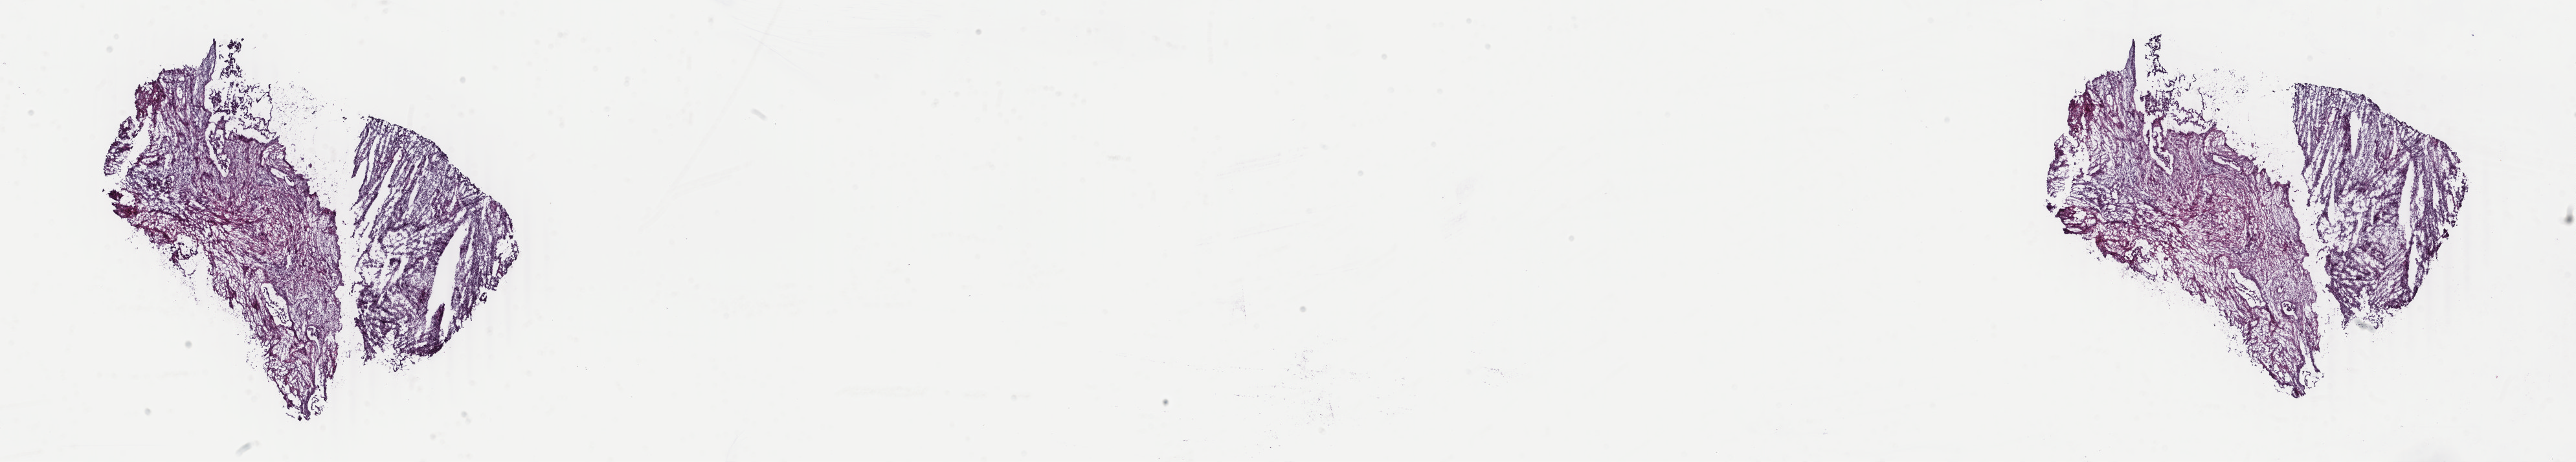
Digitized Hematoxylin and eosin (H&E) stained tissue section (whole slide) — whole scanned area (about 31.6 x 5.7 mm) shown as a low-resolution overview, frozen section from the top of the tissue portion, uterus, primary tumour sample. Patient: female, age at initial diagnosis 62 years. Slide review estimates, as recorded: tumour cells 100%, tumour nuclei 80%, normal cells 0%, stromal cells 0%, necrosis 0%. Inflammatory infiltration, as recorded: lymphocyte infiltration 1%, monocyte infiltration 0%, neutrophil infiltration 0%.
• FIGO stage: IVB
• diagnosis: Mullerian mixed tumor (myometrium)